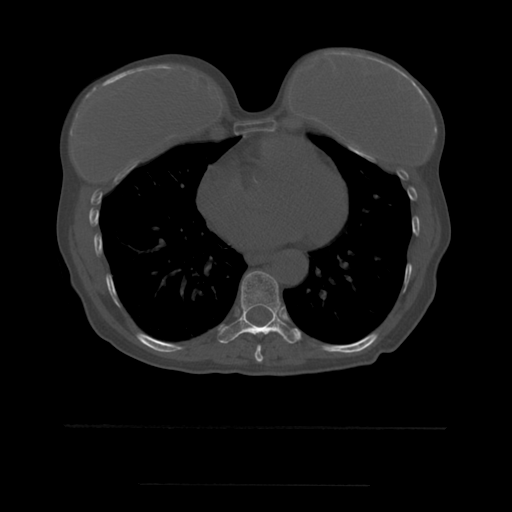
CT including the spine, one axial slice. Position 325 of 544 along the scan axis. Bone window (W 1800 / L 400 HU). 512 × 512 image matrix, field of view 350 × 350 mm. Patient age 58 years. From the clinical record (not read from this slice): primary cancer: lung.
Structures marked on this image (semi-automatically segmented with operator editing):
- T8 vertebra: bounding box [x1, y1, x2, y2] px = [255, 345, 263, 363]
- T9 vertebra: [219, 271, 302, 344]